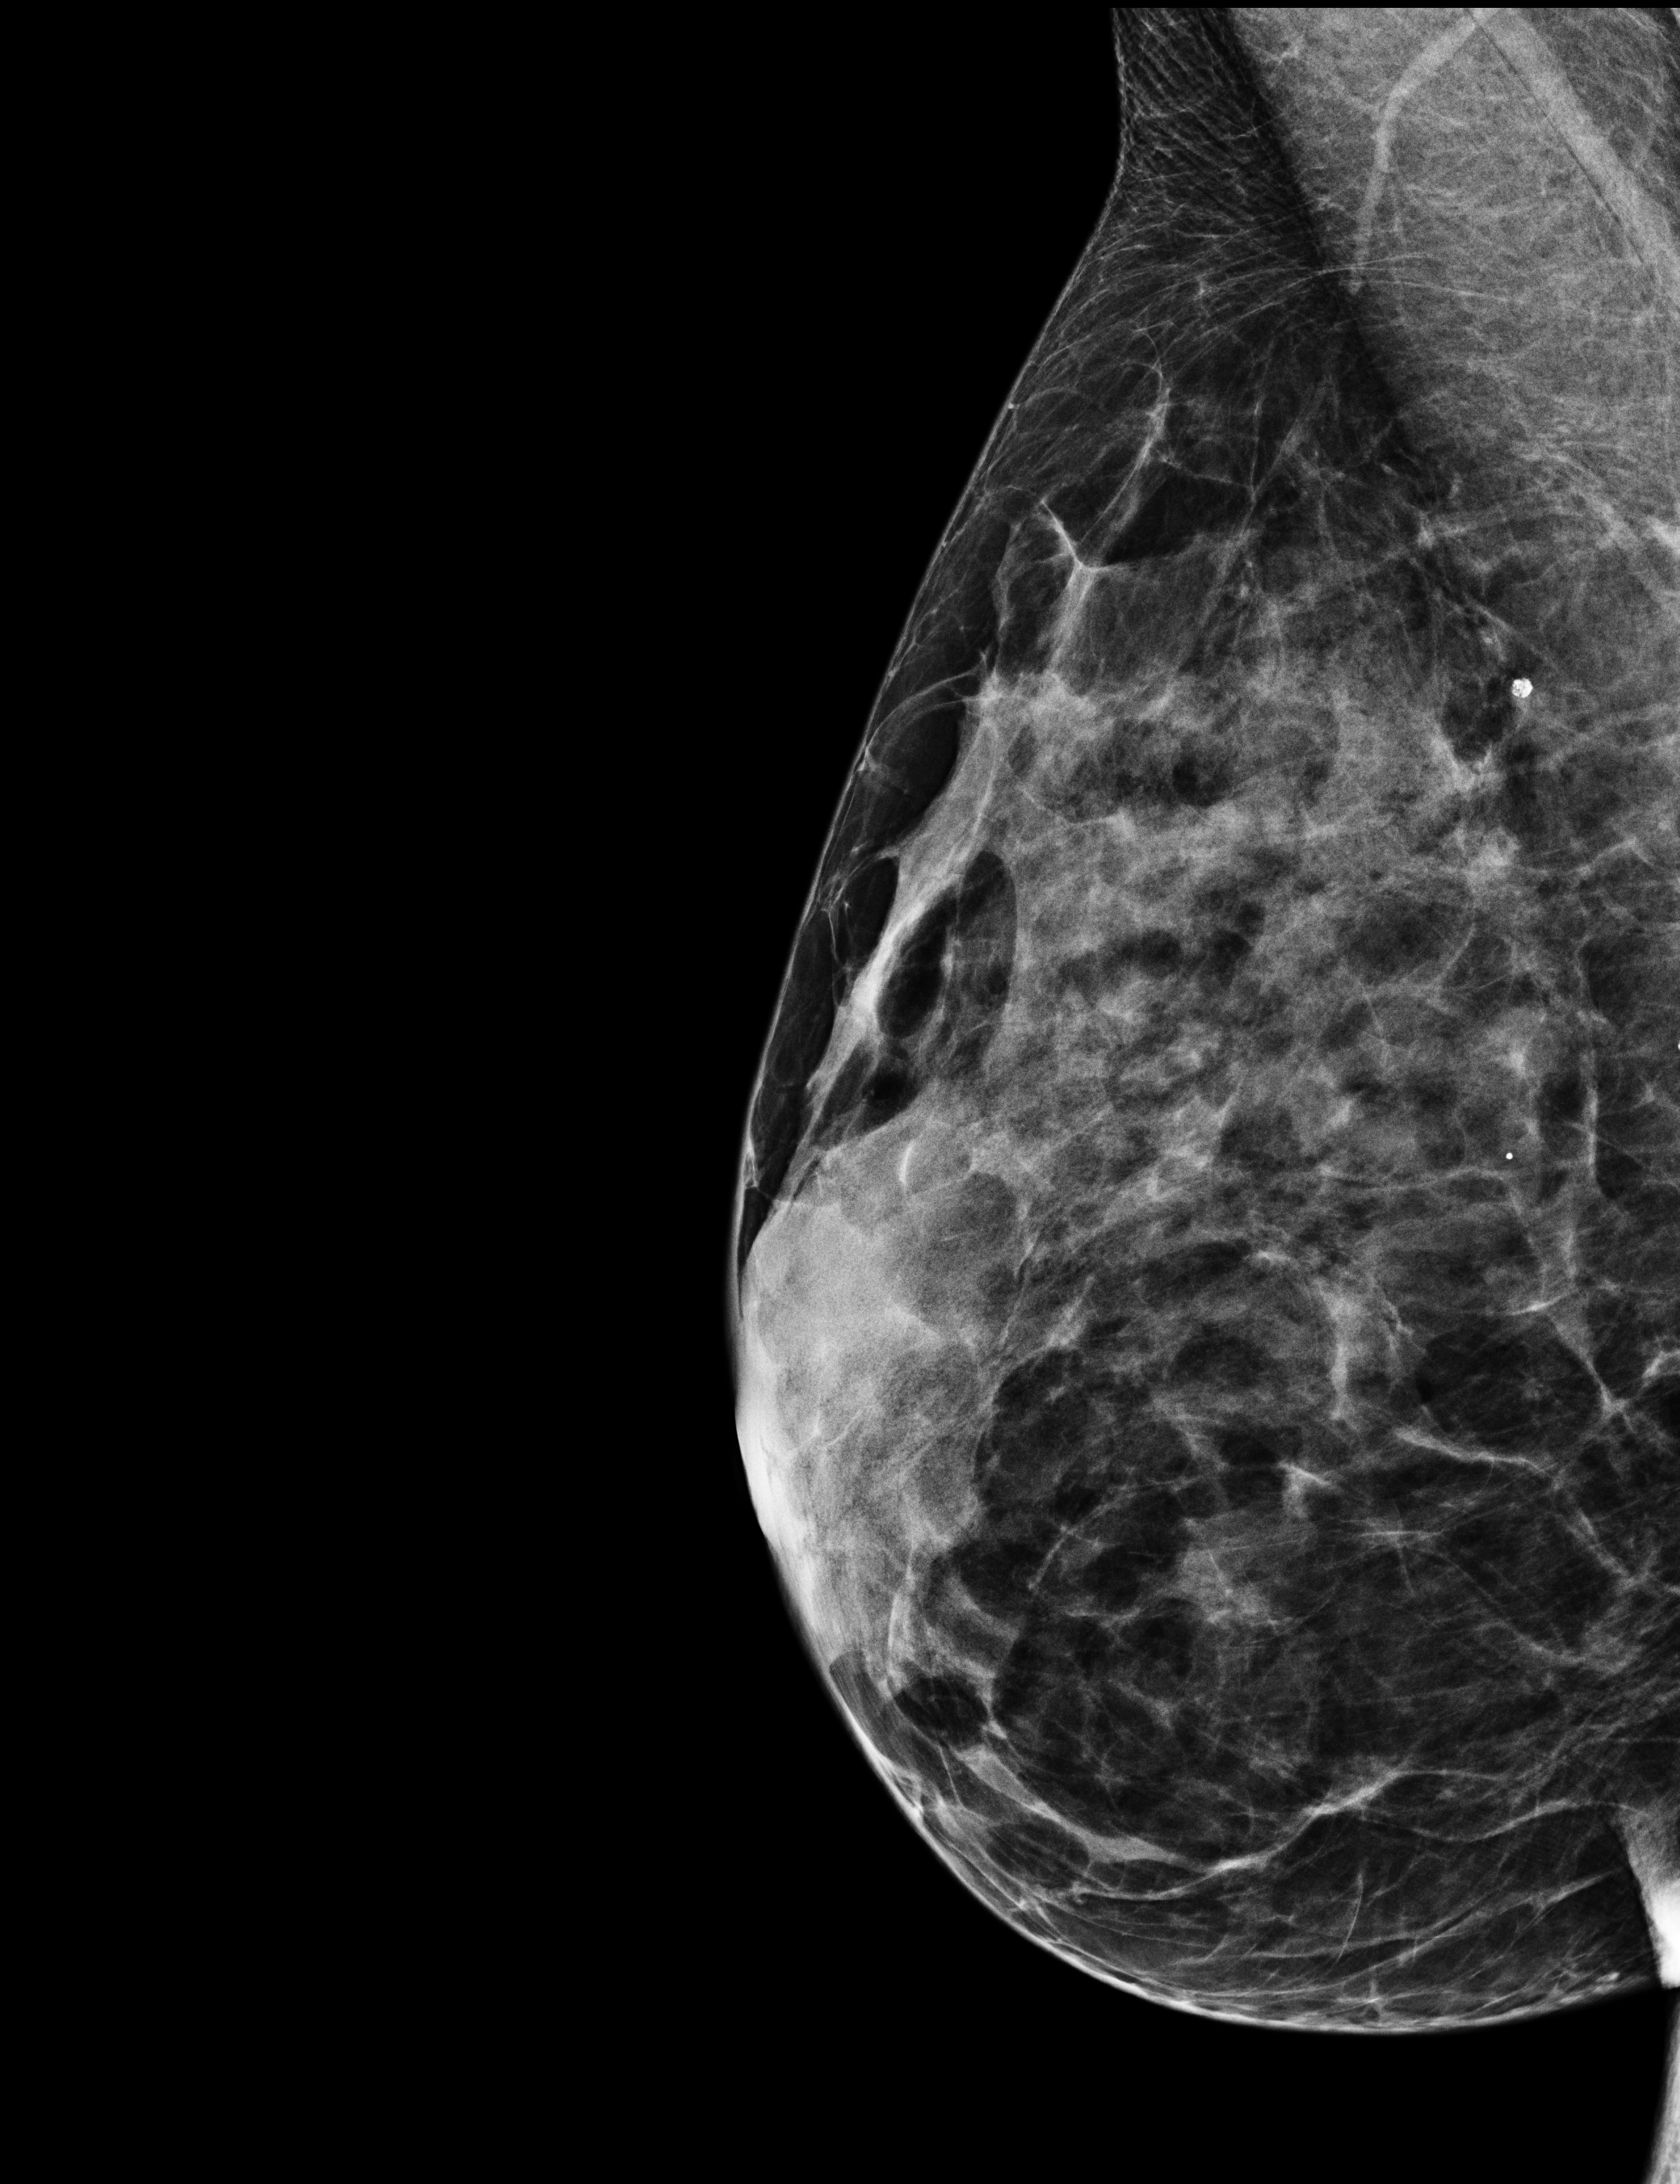
Full-field digital mammogram (FFDM); right breast; mediolateral oblique (MLO) view; screening examination; compressed breast thickness 33 mm; system: Selenia Dimensions. Female patient, age 54 years.
Breast density at the screening exam (both breasts): heterogeneously dense (BI-RADS density category c). Final BI-RADS assessment for this screening round (tomosynthesis exam, both breasts): category 1. Recall: no recall after this screen.